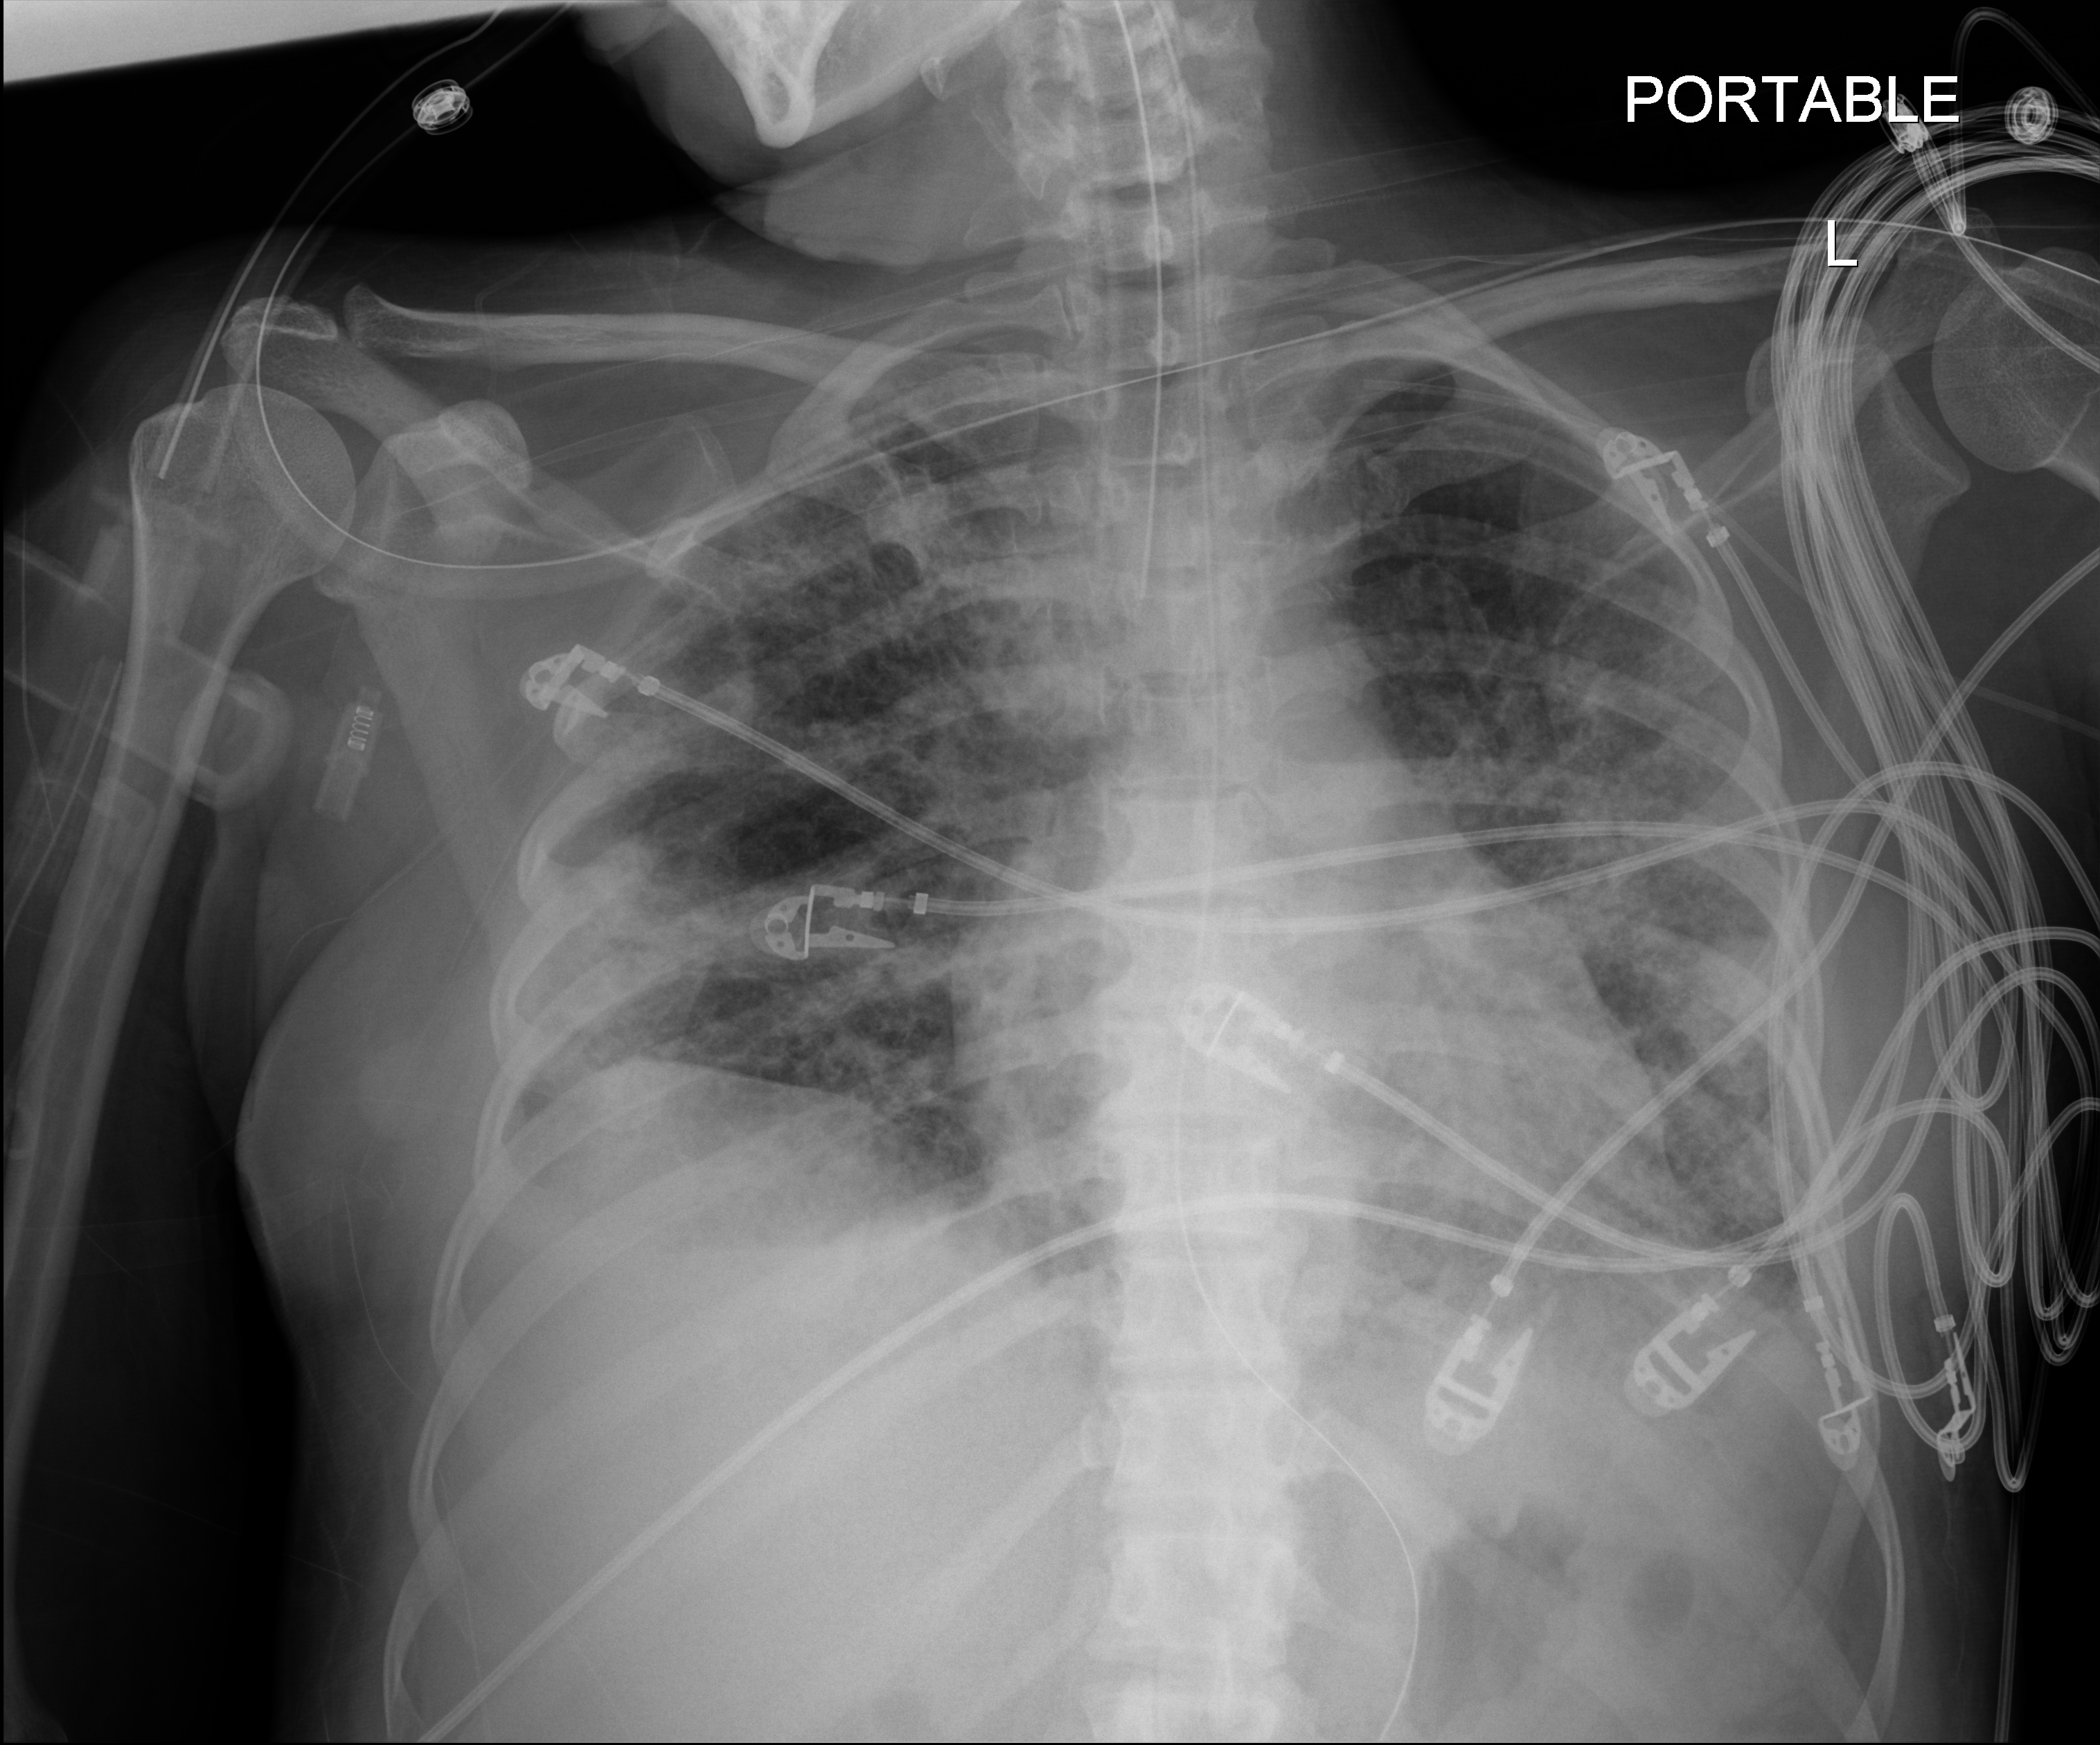
Chest X-ray (portable); anteroposterior (AP) projection. Female patient hospitalised with COVID-19, age 18–59 years.
From the hospital-stay record, not from the radiograph (when in the stay this image was taken is not recorded): diabetes (admission record): no.